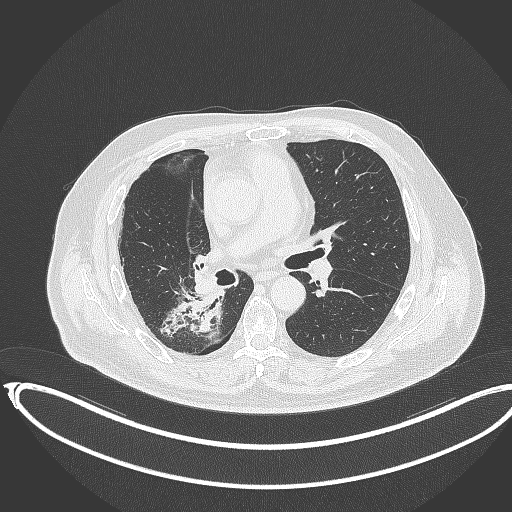
Chest CT, one axial slice; slice 192 of 403 in the series (ordered by position); lung window (W 1500 / L -600 HU); 1 mm slice thickness; 512 × 512 image matrix, field of view 436 × 436 mm. Male patient, age 68 years. Case-level facts recorded for this patient, not image findings: clinical TNM (as recorded): T2a N0 M0.
Outlined on this slice (bounding box drawn by a radiologist):
- lung tumour (recorded histology: adenocarcinoma): bounding box [x1, y1, x2, y2] px = [154, 294, 227, 344]